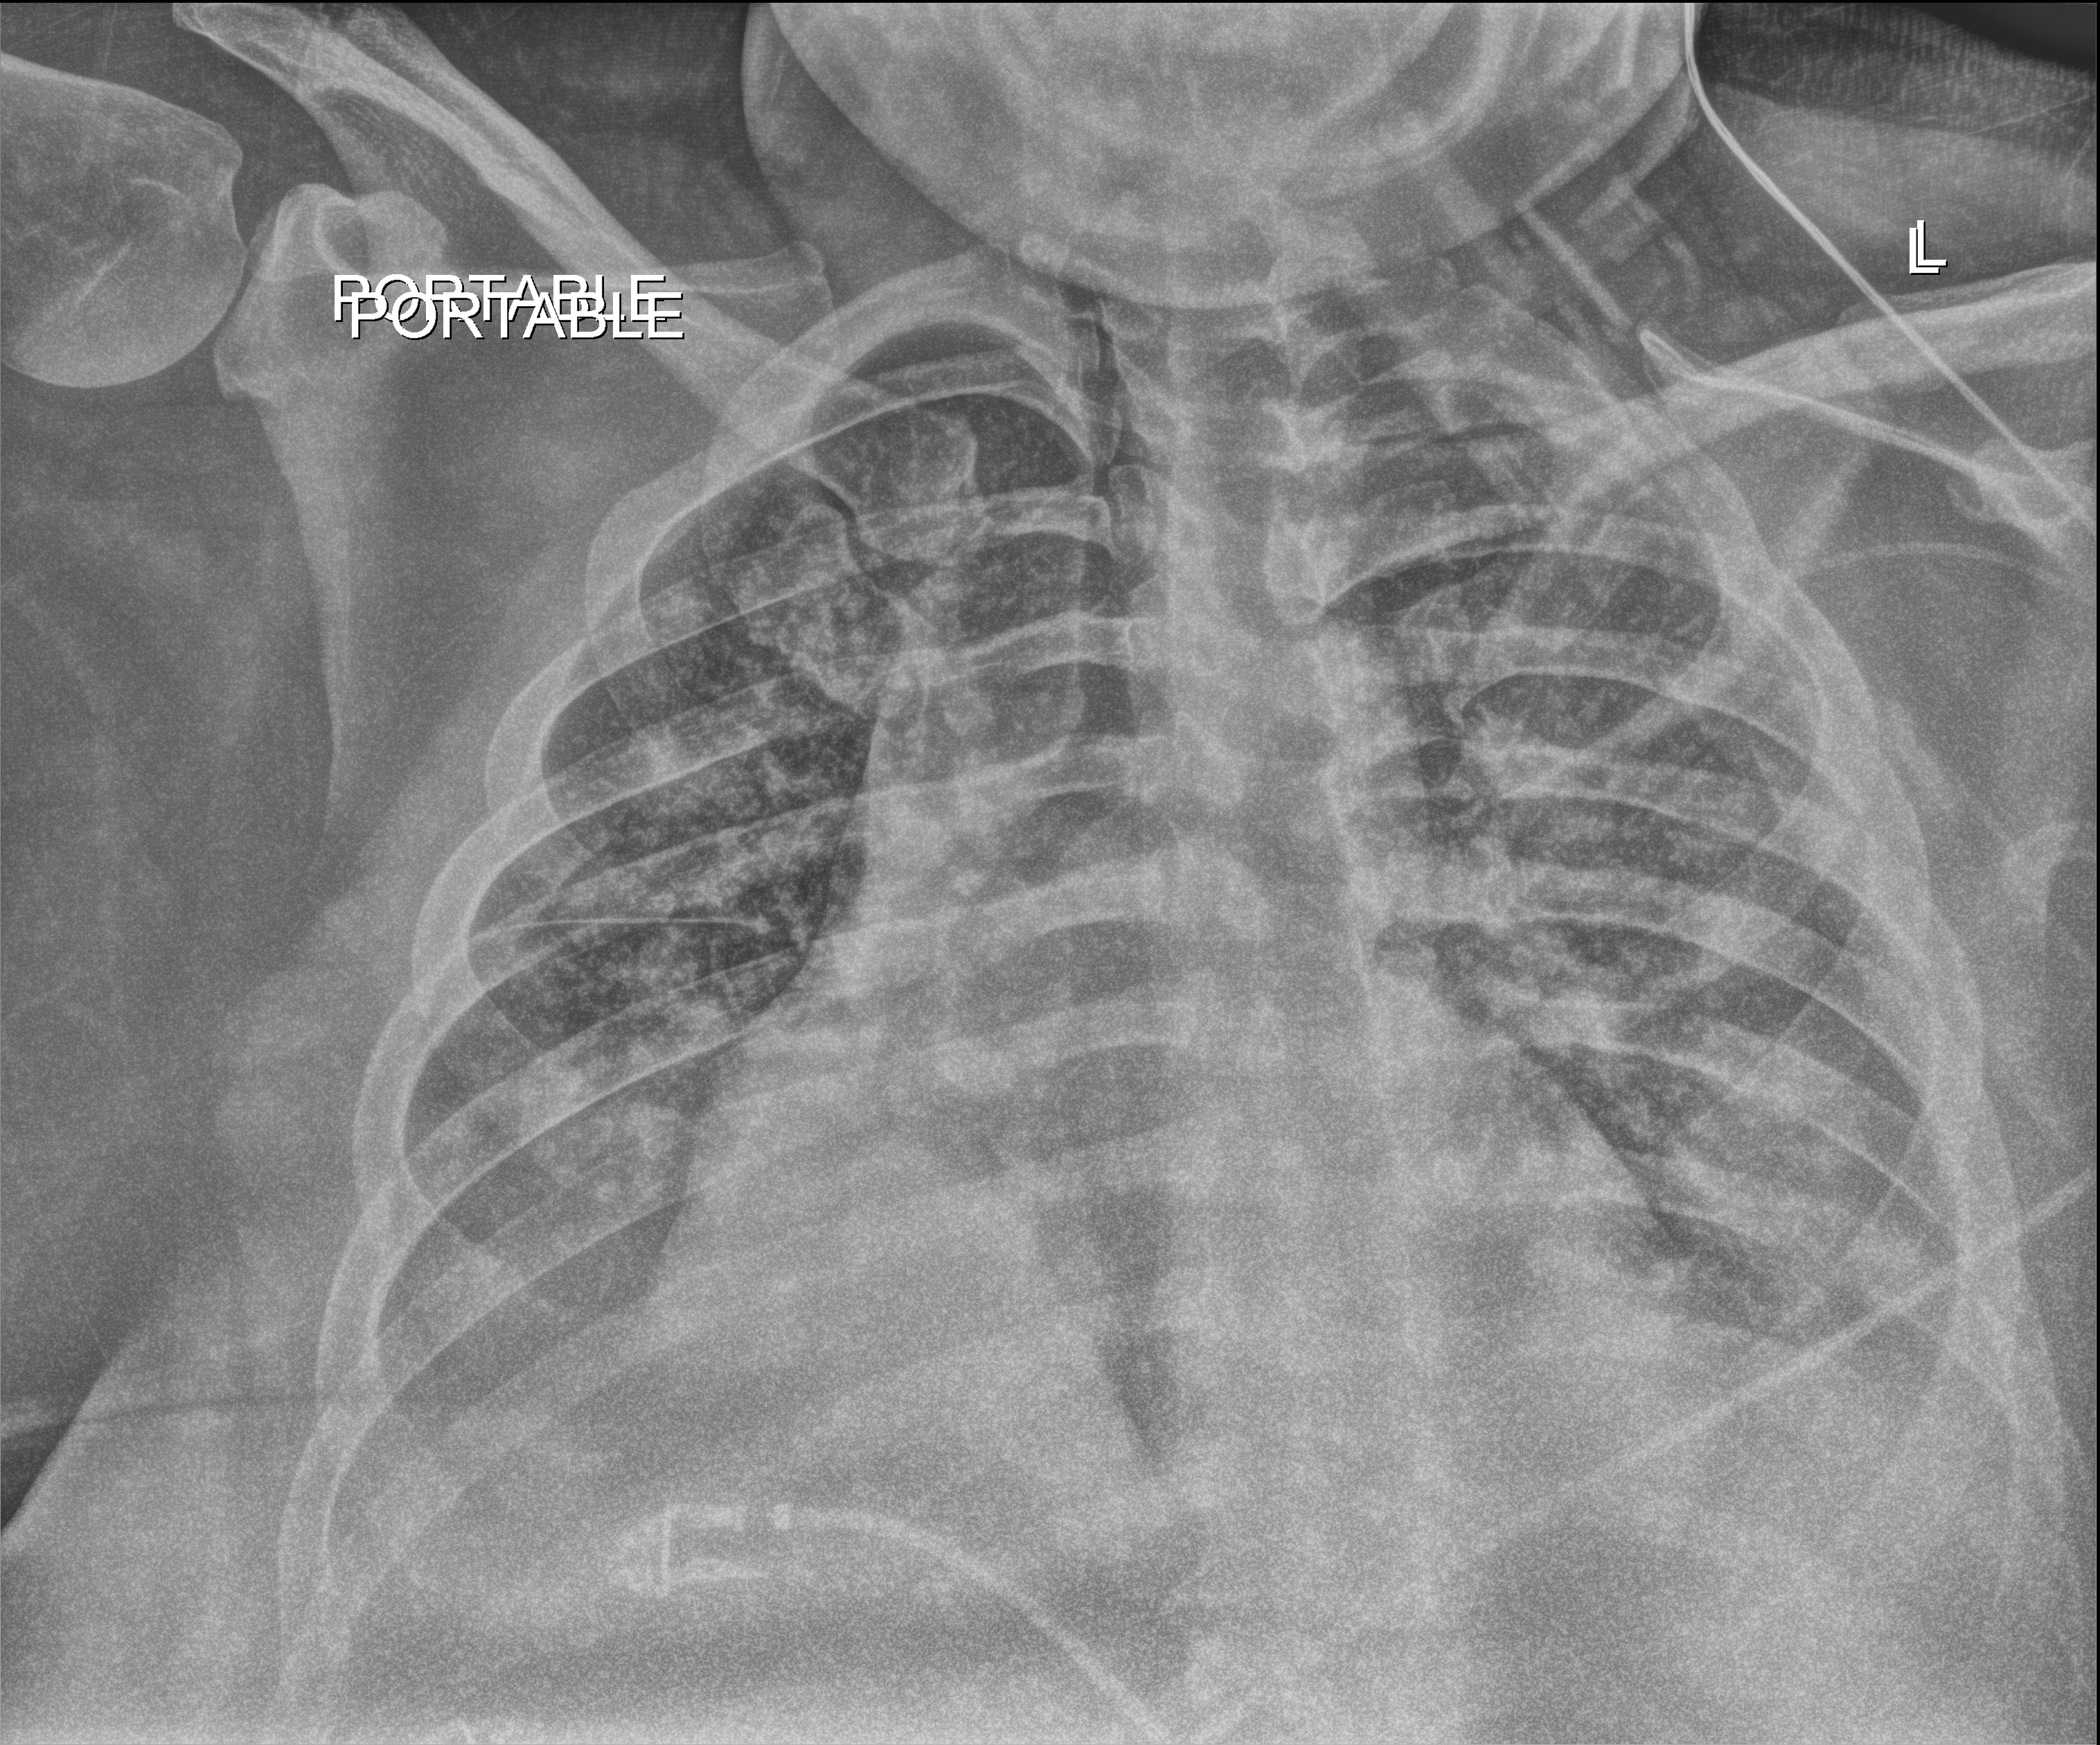
Chest radiograph (digital radiography), anteroposterior (AP) projection. Patient hospitalised with COVID-19; male, aged 18–59 years.
From the hospital-stay record, not from the radiograph (when in the stay this image was taken is not recorded): admitted to intensive care during this hospital stay: yes.